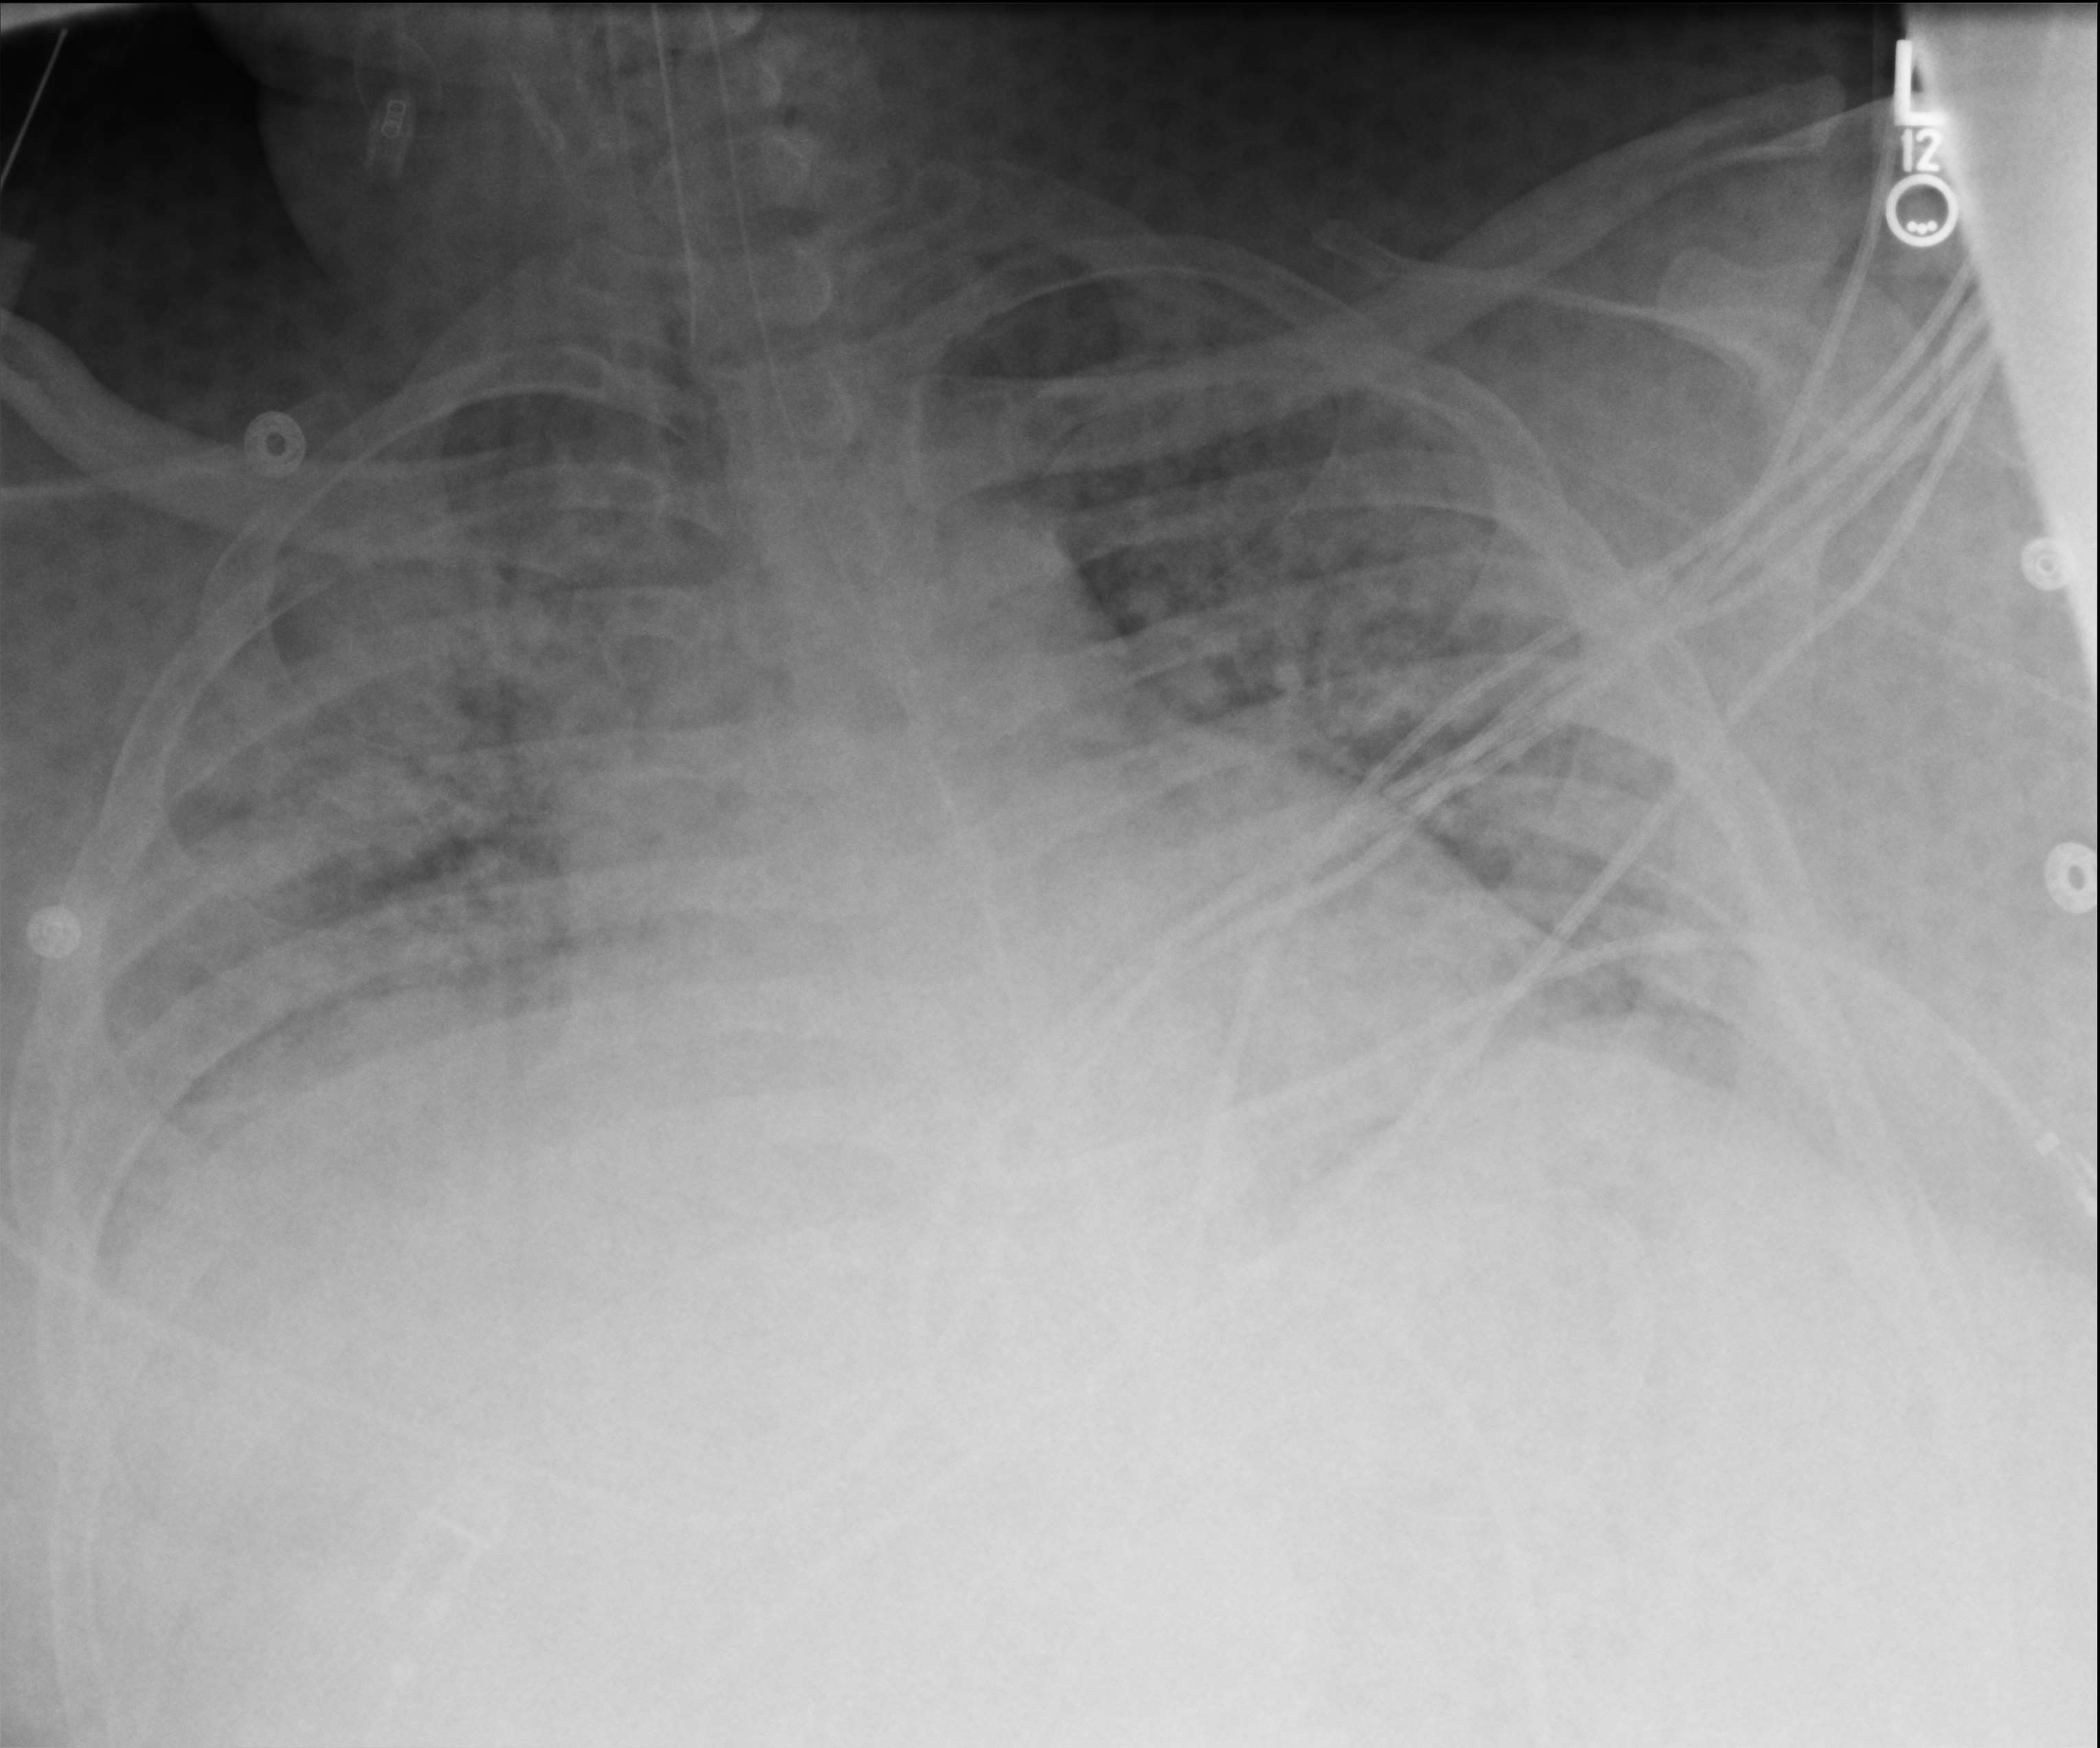
Chest X-ray (portable). Male patient hospitalised with COVID-19, age 18–59 years.
Admission-level facts for this patient (not findings on this image; timing relative to this image not recorded):
- COPD (admission record): yes
- mechanically ventilated during this hospital stay: yes
- admitted to intensive care during this hospital stay: yes